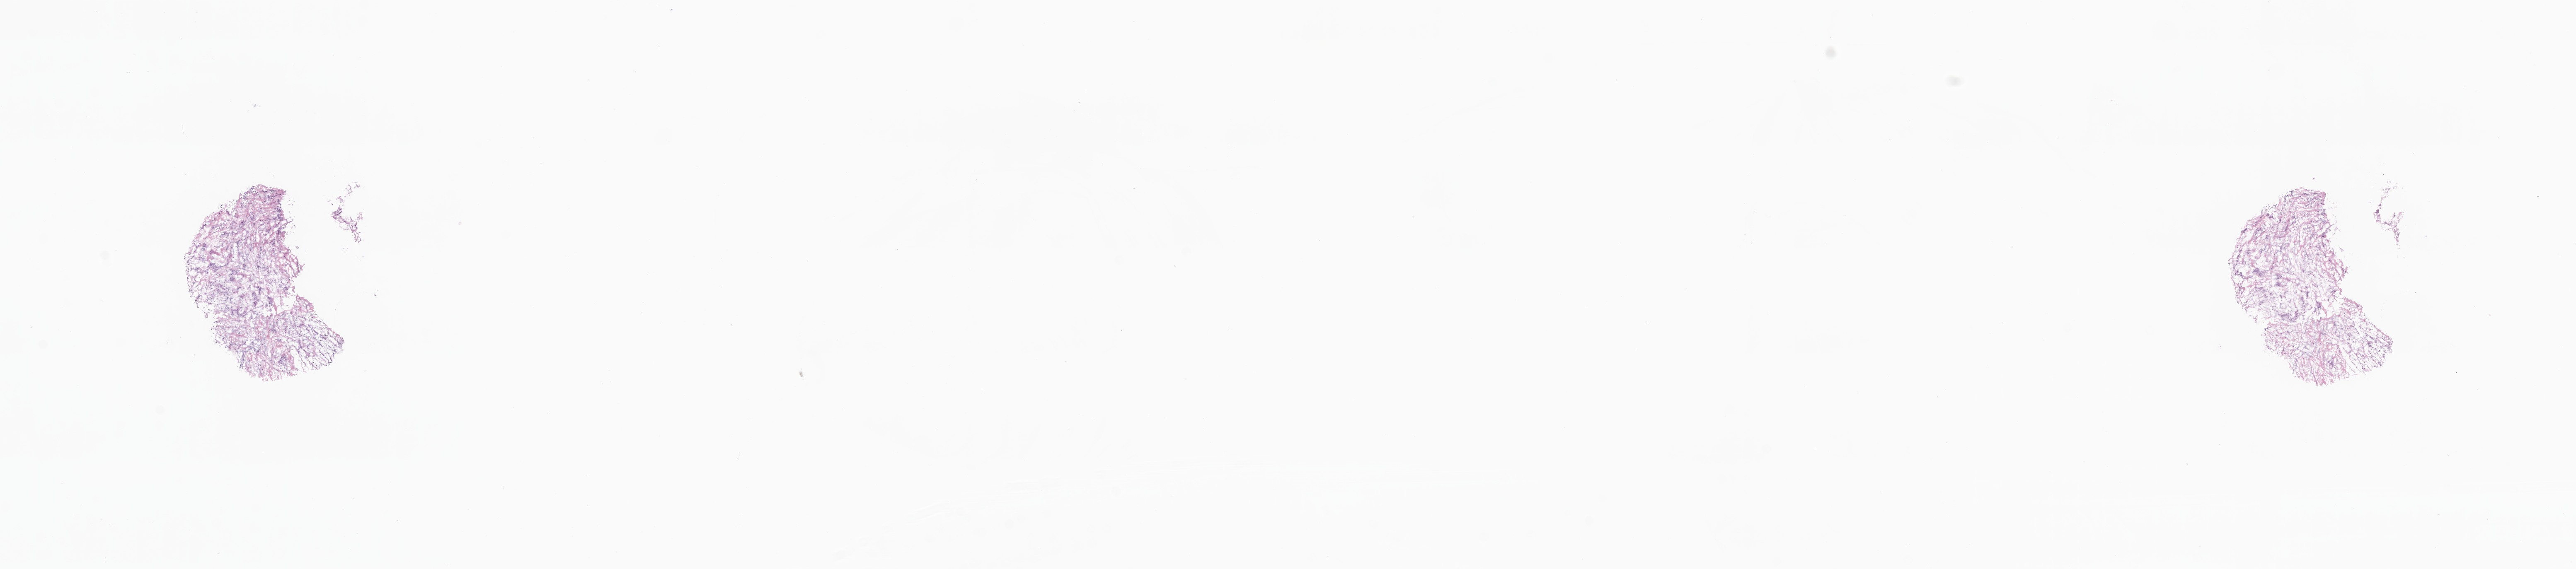
Hematoxylin and eosin (H&E) whole-slide image, shown as a low-resolution overview of the whole scanned area (about 26.2 x 5.8 mm); frozen section; primary tumor; site: breast (right). Female patient; age at initial diagnosis 67 years. Pathologist review of this section (percent, as recorded): tumor cells 20%, tumor nuclei 30%, stromal cells 80%, necrosis 0%, normal cells 0%. Inflammatory infiltration, as recorded: lymphocyte infiltration 0%, monocyte infiltration 0%, neutrophil infiltration 0%.
Diagnosis: Infiltrating duct carcinoma, NOS. Section: top of the tissue portion.